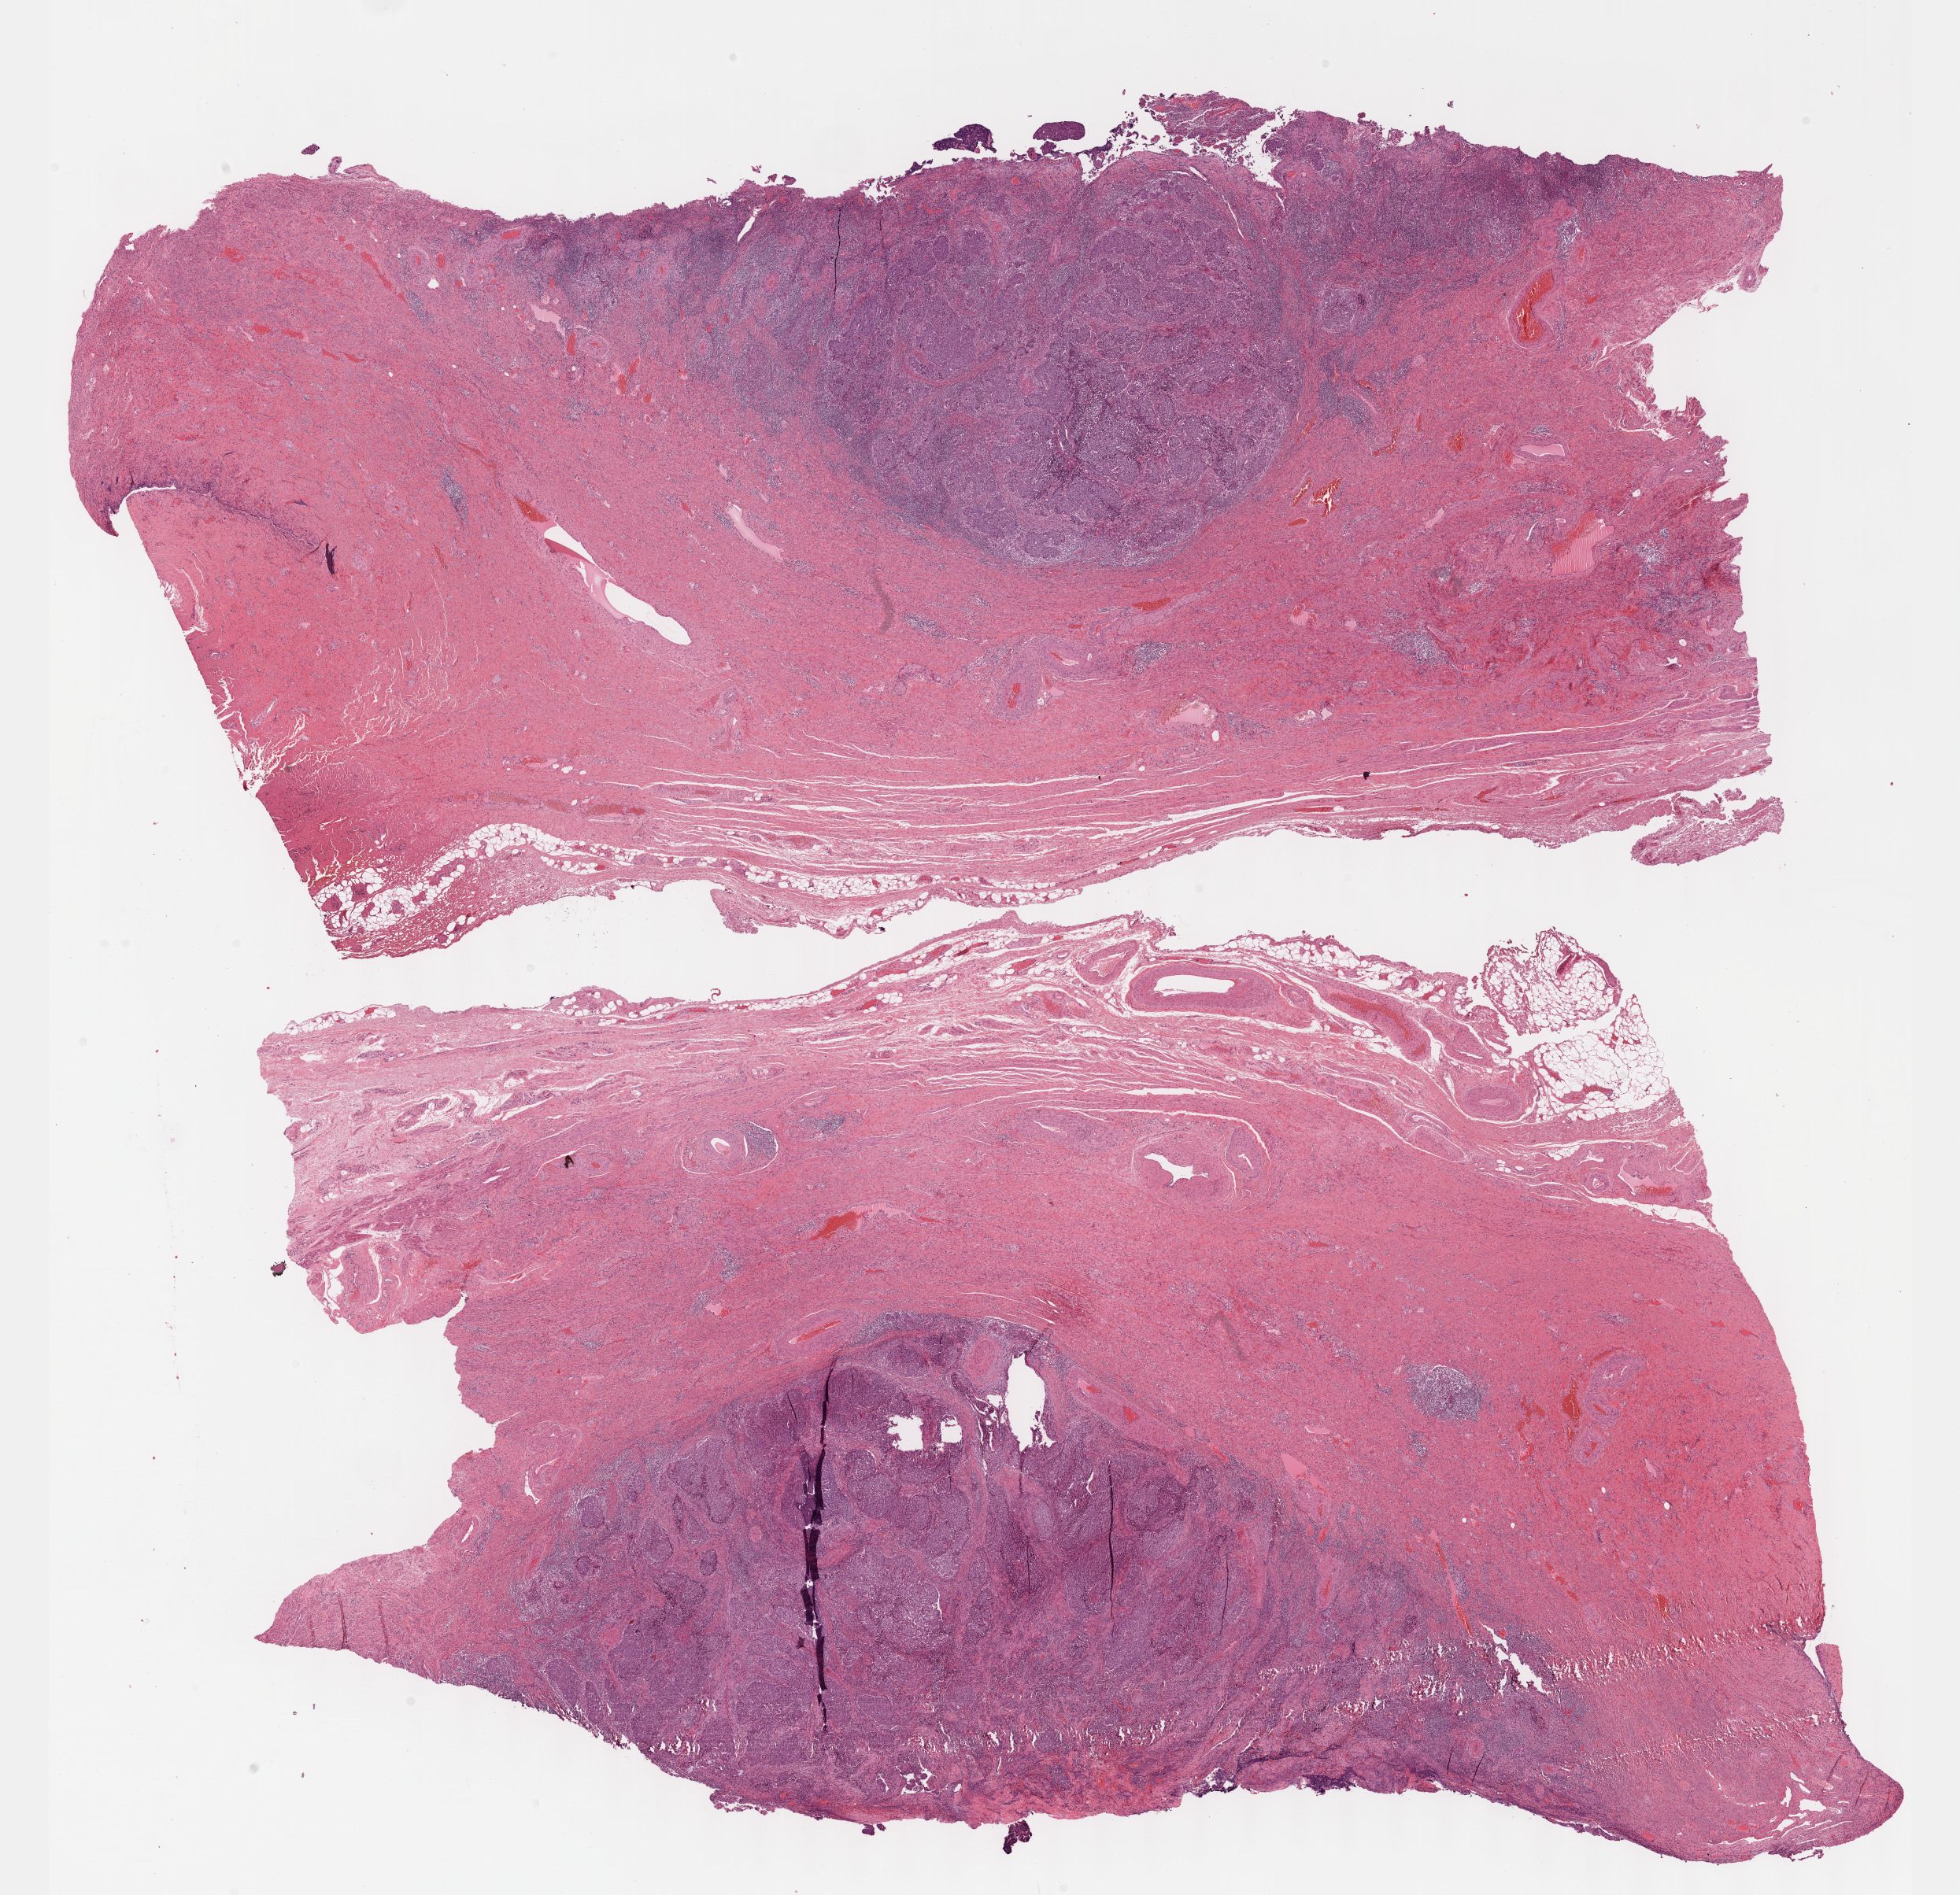
Digitized H&E-stained tissue section (whole slide) — whole scanned area (about 20.1 x 19.5 mm, slide scanned at 40x) shown as a low-resolution overview, FFPE section, sample: primary tumour, cervix. Female patient; age at initial diagnosis 44 years.
Pathologic diagnosis: Squamous cell carcinoma, NOS (cervix uteri).